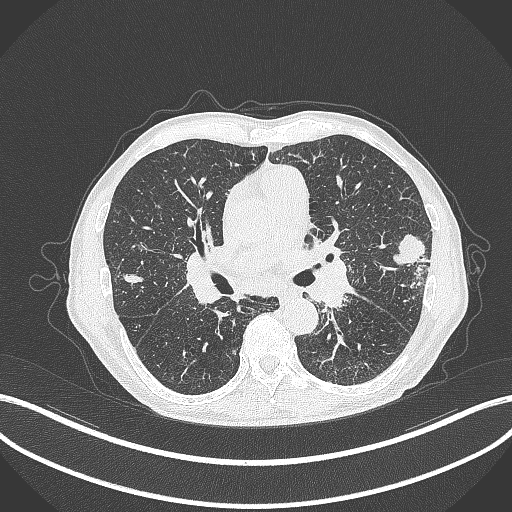
Chest CT, one axial slice. Slice 225 of 463 in the series (ordered by position). Reconstruction kernel B70f. 120 kVp. Lung window (W 1500 / L -600 HU). 1 mm slice thickness. 512 × 512 image matrix, field of view 400 × 400 mm. Patient: male, 74 years. Case-level facts recorded for this patient, not image findings: clinical TNM (as recorded): T2a N1 M0.
Outlined on this slice (bounding box drawn by a radiologist):
- lung tumour (recorded histology: adenocarcinoma): bounding box (x1, y1, x2, y2) in pixels: (387, 231, 436, 271)